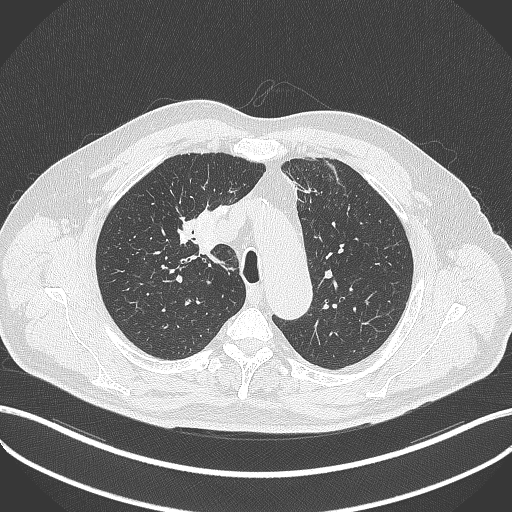
Chest CT, one axial slice. Position 293 of 411 along the scan axis. Reconstruction kernel B70f. 120 kVp. Lung window (W 1500 / L -600 HU). 512 × 512 image matrix, field of view 400 × 400 mm. Patient: male, 60 years. Case-level facts recorded for this patient, not image findings: clinical TNM (as recorded): T1b N1 M0.
Outlined on this slice (rectangle marked by the reading radiologist):
- lung tumour (recorded histology: squamous cell carcinoma): bounding box <195,208,220,256> (left, top, right, bottom; pixels)